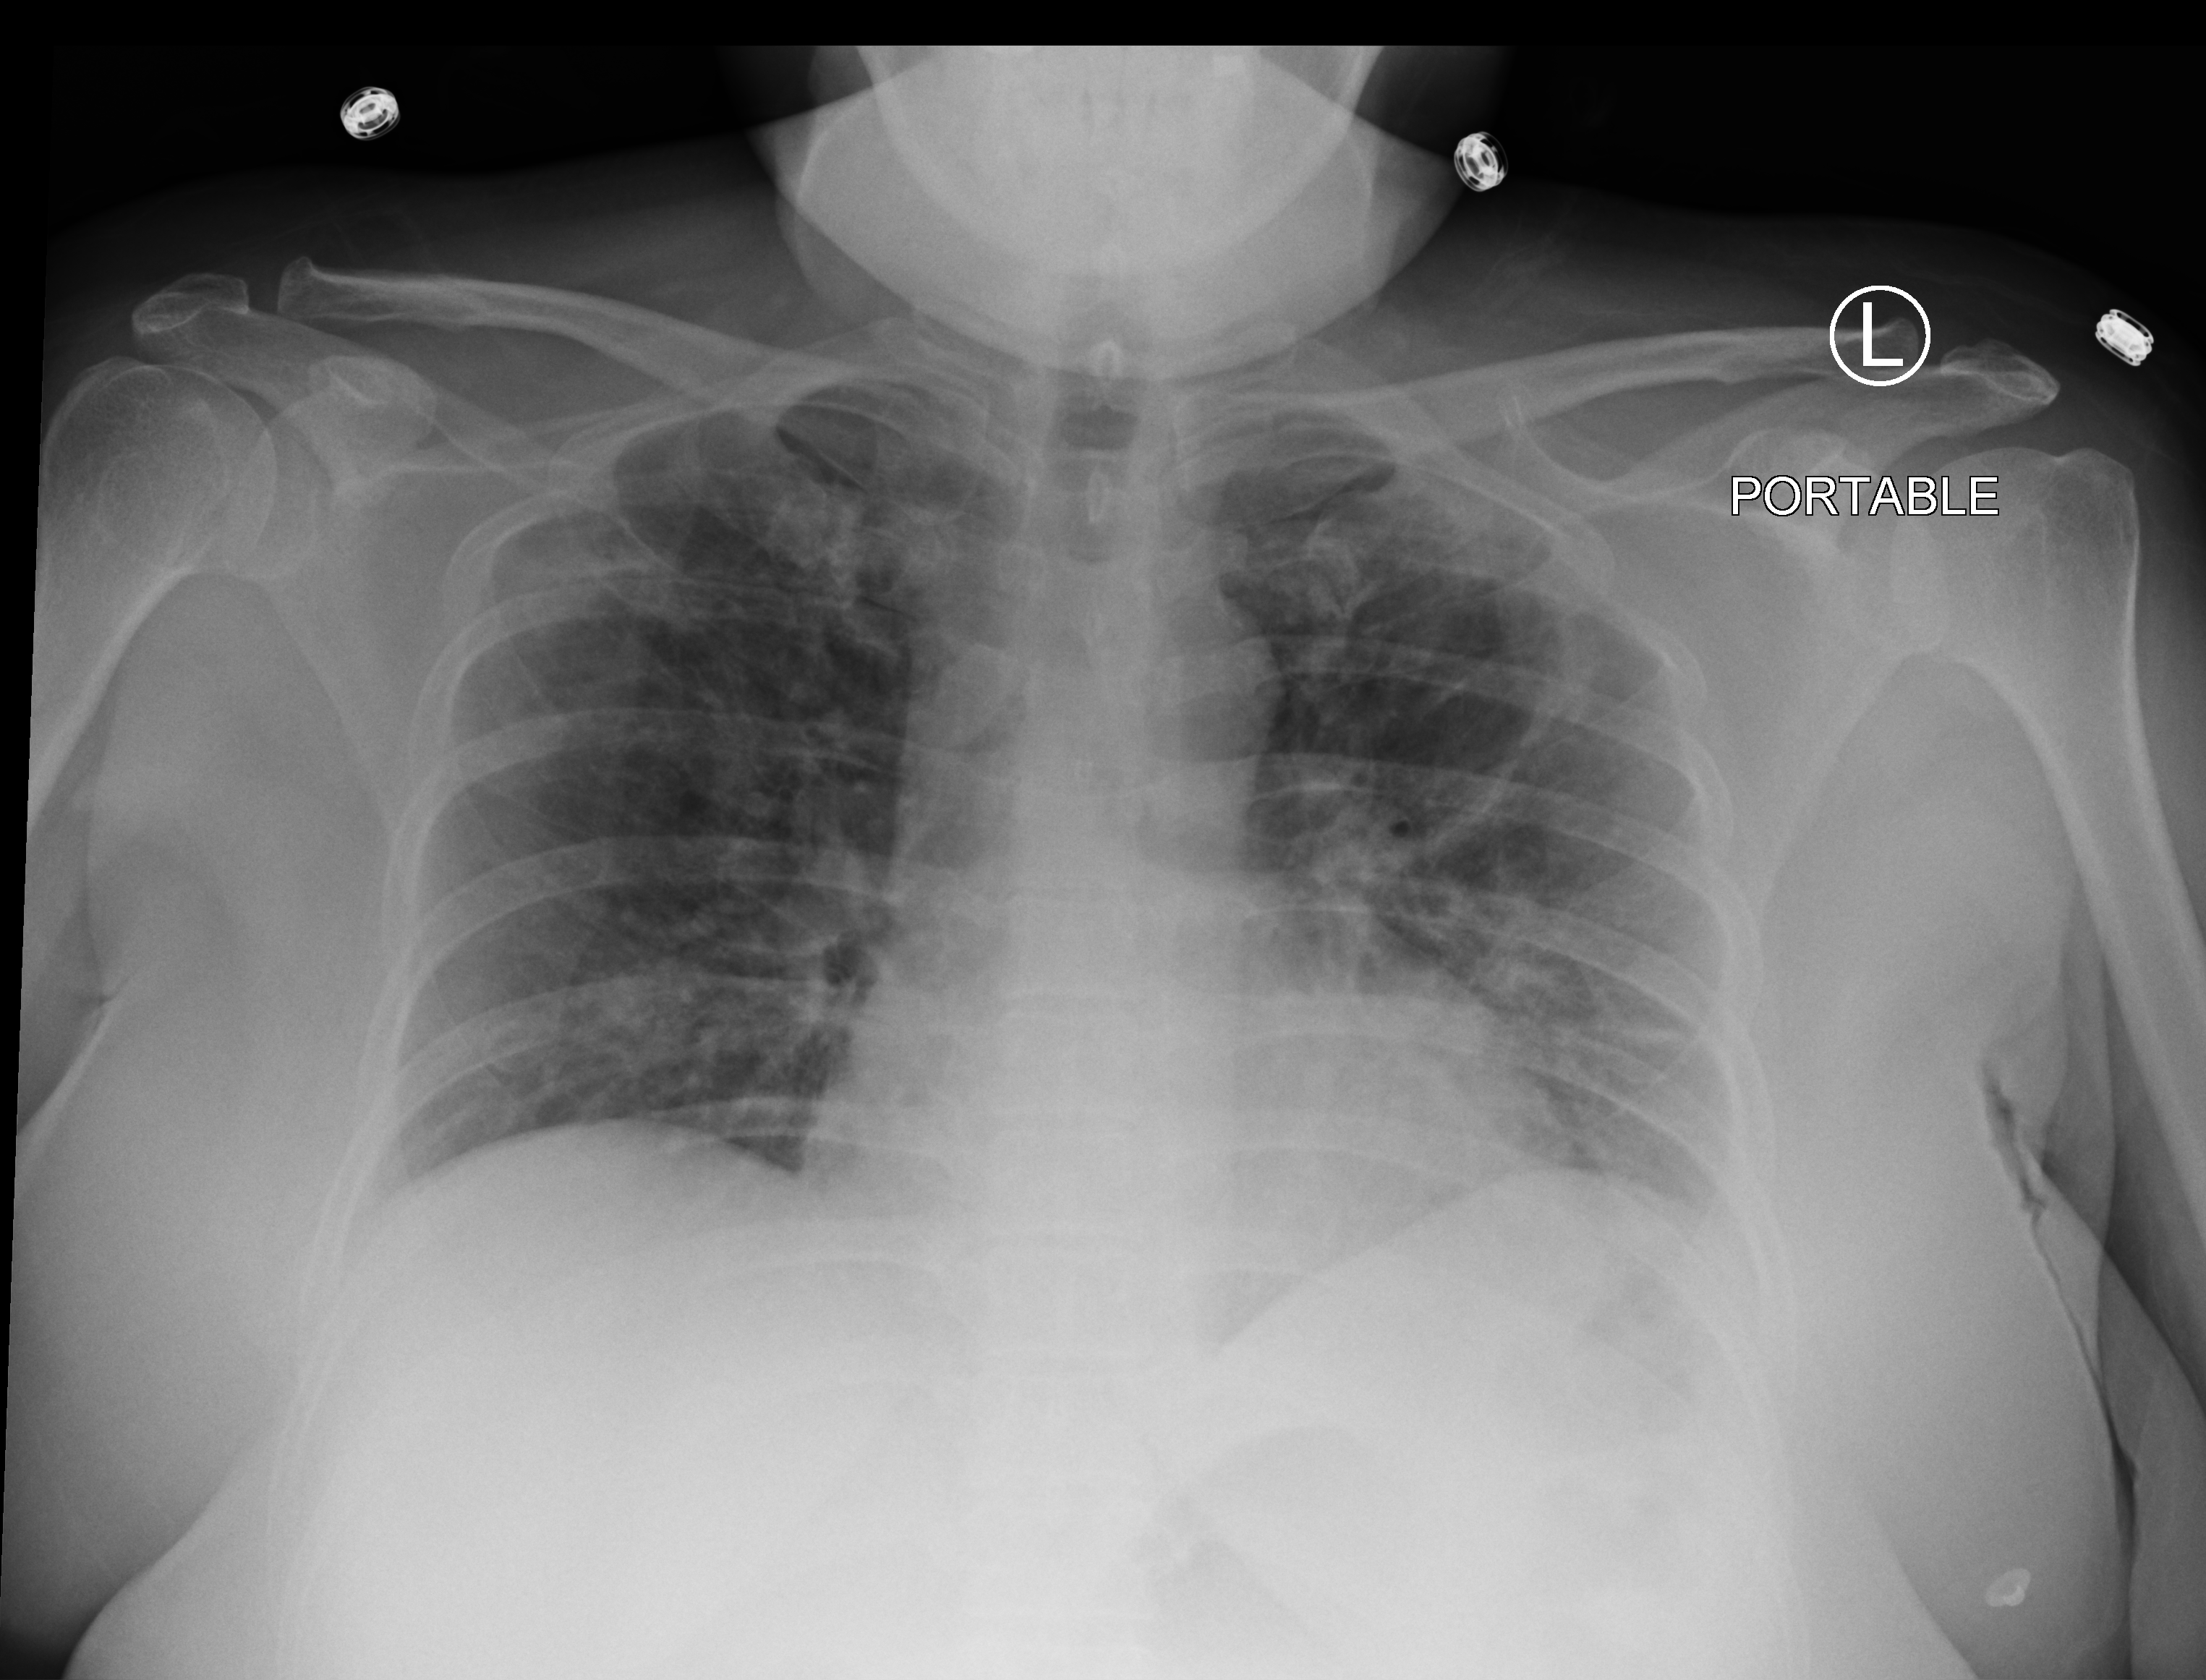
Chest X-ray (portable); anteroposterior (AP) projection. Patient hospitalised with COVID-19; female, aged 18–59 years.
Admission-level facts for this patient (not findings on this image; timing relative to this image not recorded):
- admitted to intensive care during this hospital stay: yes